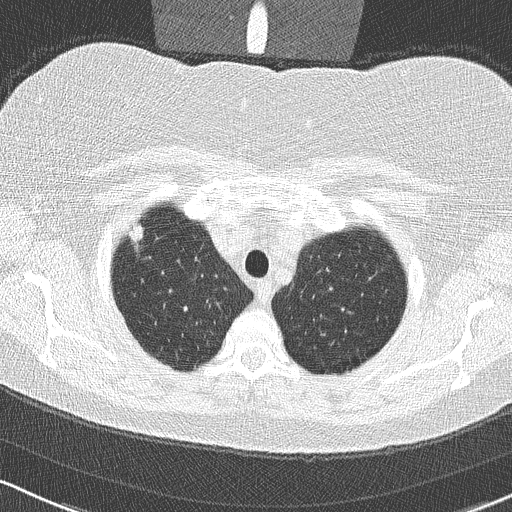
Chest CT (low-dose screening protocol), one axial image. Third annual screen. Lung window (W 1500 / L -600 HU). 2 mm slice thickness. Lung (sharp) reconstruction kernel (B50f). Slice 43 of 315 in the series. Female, age 58 years at enrolment. Former smoker at enrolment.
Lesion marked by an expert reader, box from (x=118, y=219) to (x=158, y=260) px. The screening reader recorded 2 non-calcified nodules or masses ≥4 mm on this exam (right upper lobe, right lower lobe); which of them this box marks is not recorded. Participant outcome: lung cancer diagnosed 48 days after this screen — bronchiolo-alveolar adenocarcinoma, NOS, right upper lobe, well differentiated (G1), stage IA (AJCC 6th edition), 9 mm at pathology.